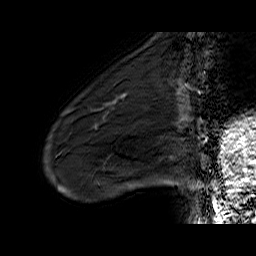
Breast MRI (dynamic contrast-enhanced), one sagittal slice; slice 15 of 60 in the series (ordered by position); dynamic contrast-enhanced series, time point 2 of 6 at this slice position (early post-contrast); 1.5 T; TE 6.5 ms, TR 32.9 ms; 4 mm slice thickness; 256 × 256 image matrix, field of view 200 × 200 mm. Female patient. From the clinical record (not read from this slice): setting: breast cancer imaged before/during neoadjuvant chemotherapy; receptor status: HER2-positive.
Annotated regions visible in this slice (semi-automatically segmented with operator editing):
- analysis volume of interest (the breast-tissue region the enhancement analysis was run in; not a lesion): bounding box [x1, y1, x2, y2] px = [72, 88, 133, 137]
- tumour enhancement mask (voxels above the 100 % enhancement threshold inside the analysis volume of interest): [95, 95, 125, 129]